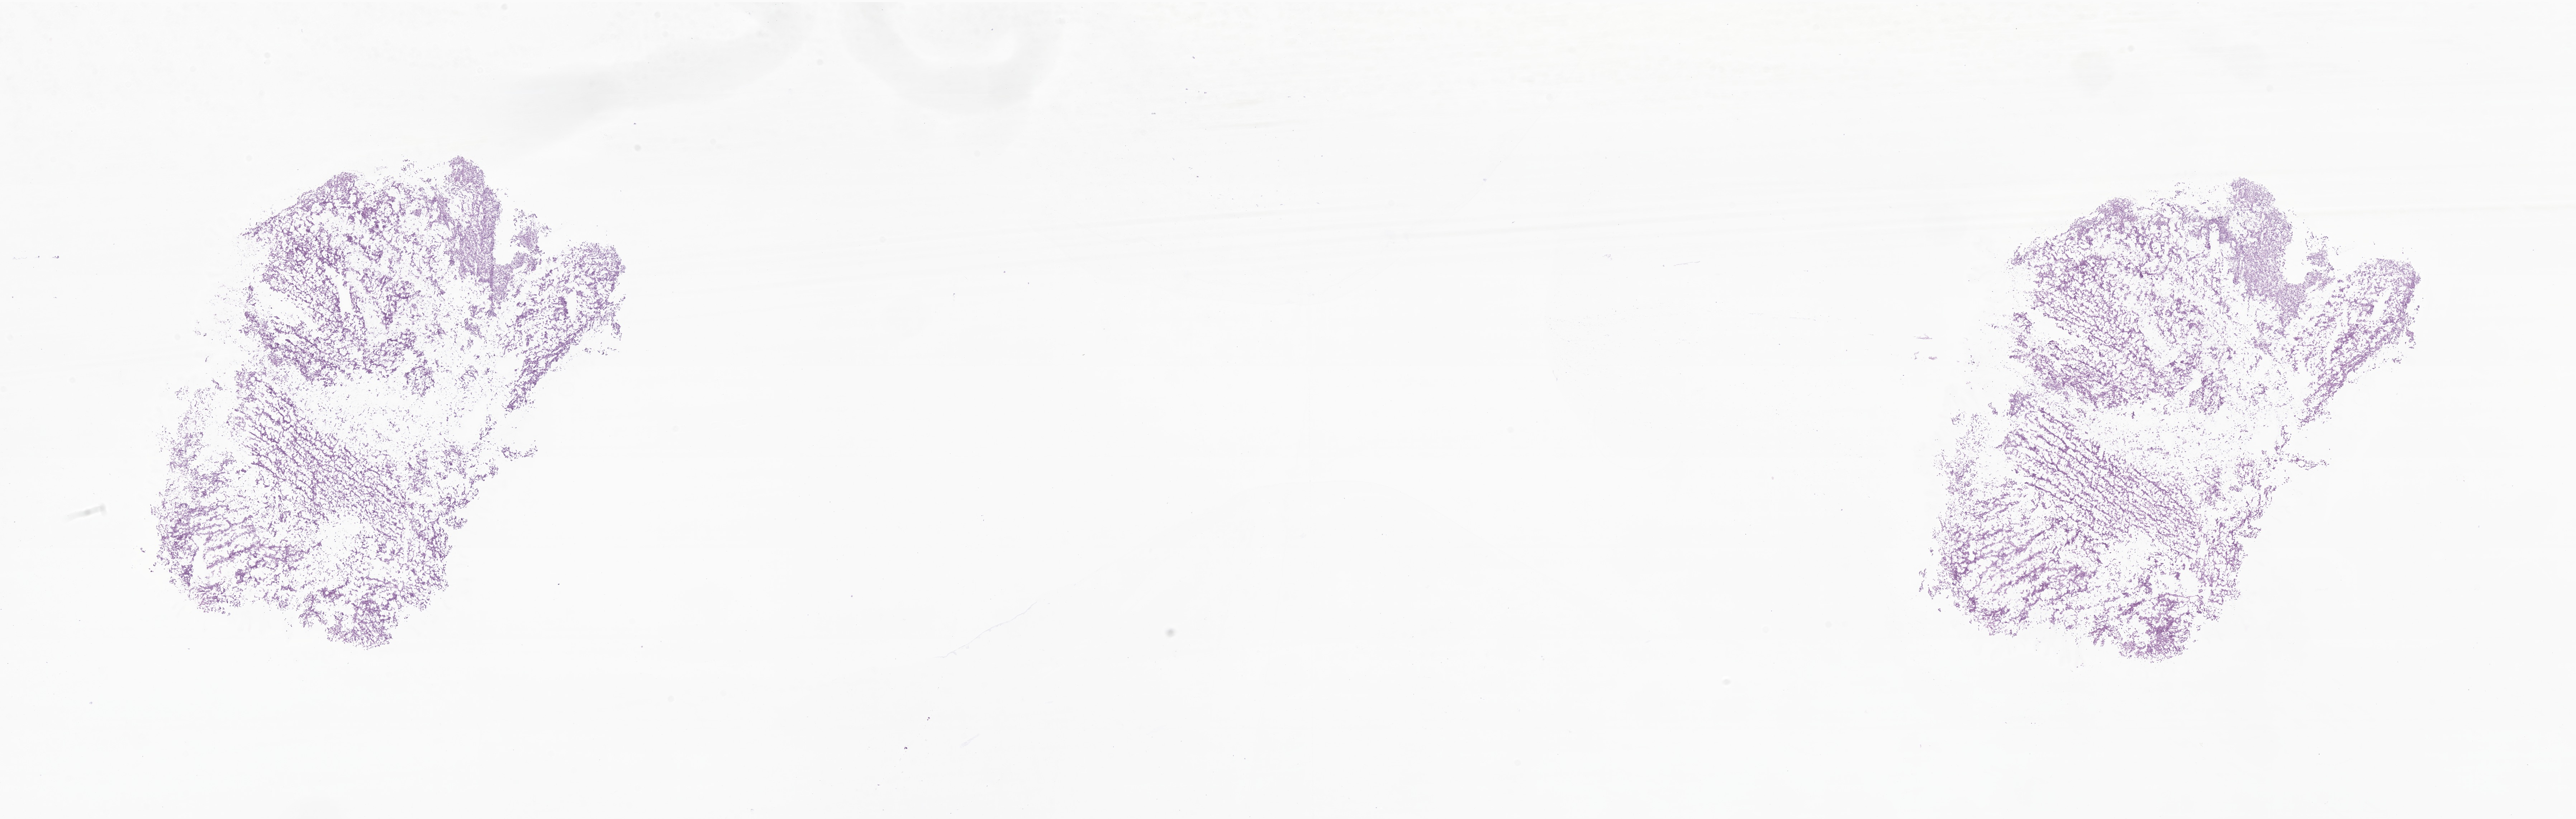
Digitized hematoxylin and eosin (H&E)-stained section of tumor tissue from the brain, low-resolution overview of the scanned area, about 30.3 x 9.6 mm, cryosection (OCT / tissue freezing medium). Patient: male, age 74 days.
Diagnosis: Glioma, malignant.